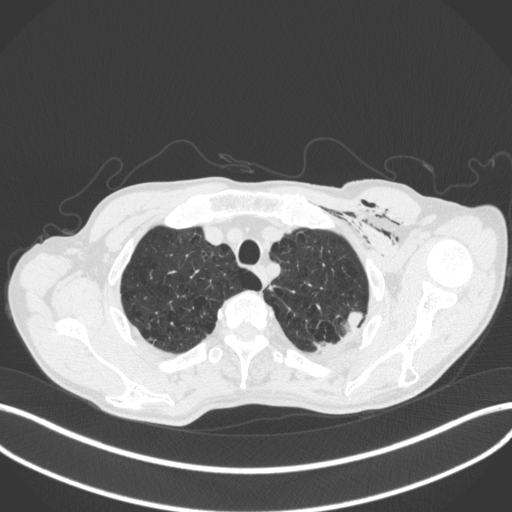
Chest CT, one axial slice; slice 356 of 416 in the series (ordered by position); 120 kVp; lung window (W 1500 / L -600 HU); 1 mm slice thickness; 512 × 512 image matrix, field of view 400 × 400 mm. Male patient, age 58 years. From the clinical record (not read from this slice): clinical TNM (as recorded): T3 N0 M0.
Outlined on this slice (bounding box drawn by a radiologist):
- lung tumour (recorded histology: adenocarcinoma): bounding box (x1, y1, x2, y2) in pixels: (341, 310, 362, 330)